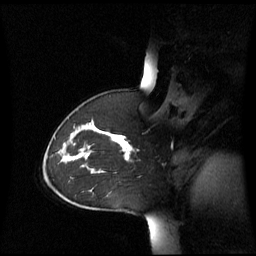
Breast MRI (dynamic contrast-enhanced), one sagittal slice; slice 43 of 60 in the series (ordered by position); dynamic contrast-enhanced series, image 2 of 3 at this slice position (ordered by acquisition); 1.5 T; TE 4.2 ms, TR 8.4 ms; 2.8 mm slice thickness; 256 × 256 image matrix. Patient: female, 43 years. From the clinical record (not read from this slice): setting: breast cancer imaged before/during neoadjuvant chemotherapy; receptor status: triple-negative.
Annotated regions visible in this slice (semi-automatic segmentation, software-assisted and operator-edited):
- analysis volume of interest (the breast-tissue region the enhancement analysis was run in; not a lesion): bounding box (x1, y1, x2, y2) in pixels: (55, 124, 134, 173)
- tumour enhancement mask (voxels above the 70 % enhancement threshold inside the analysis volume of interest): (70, 134, 133, 160)